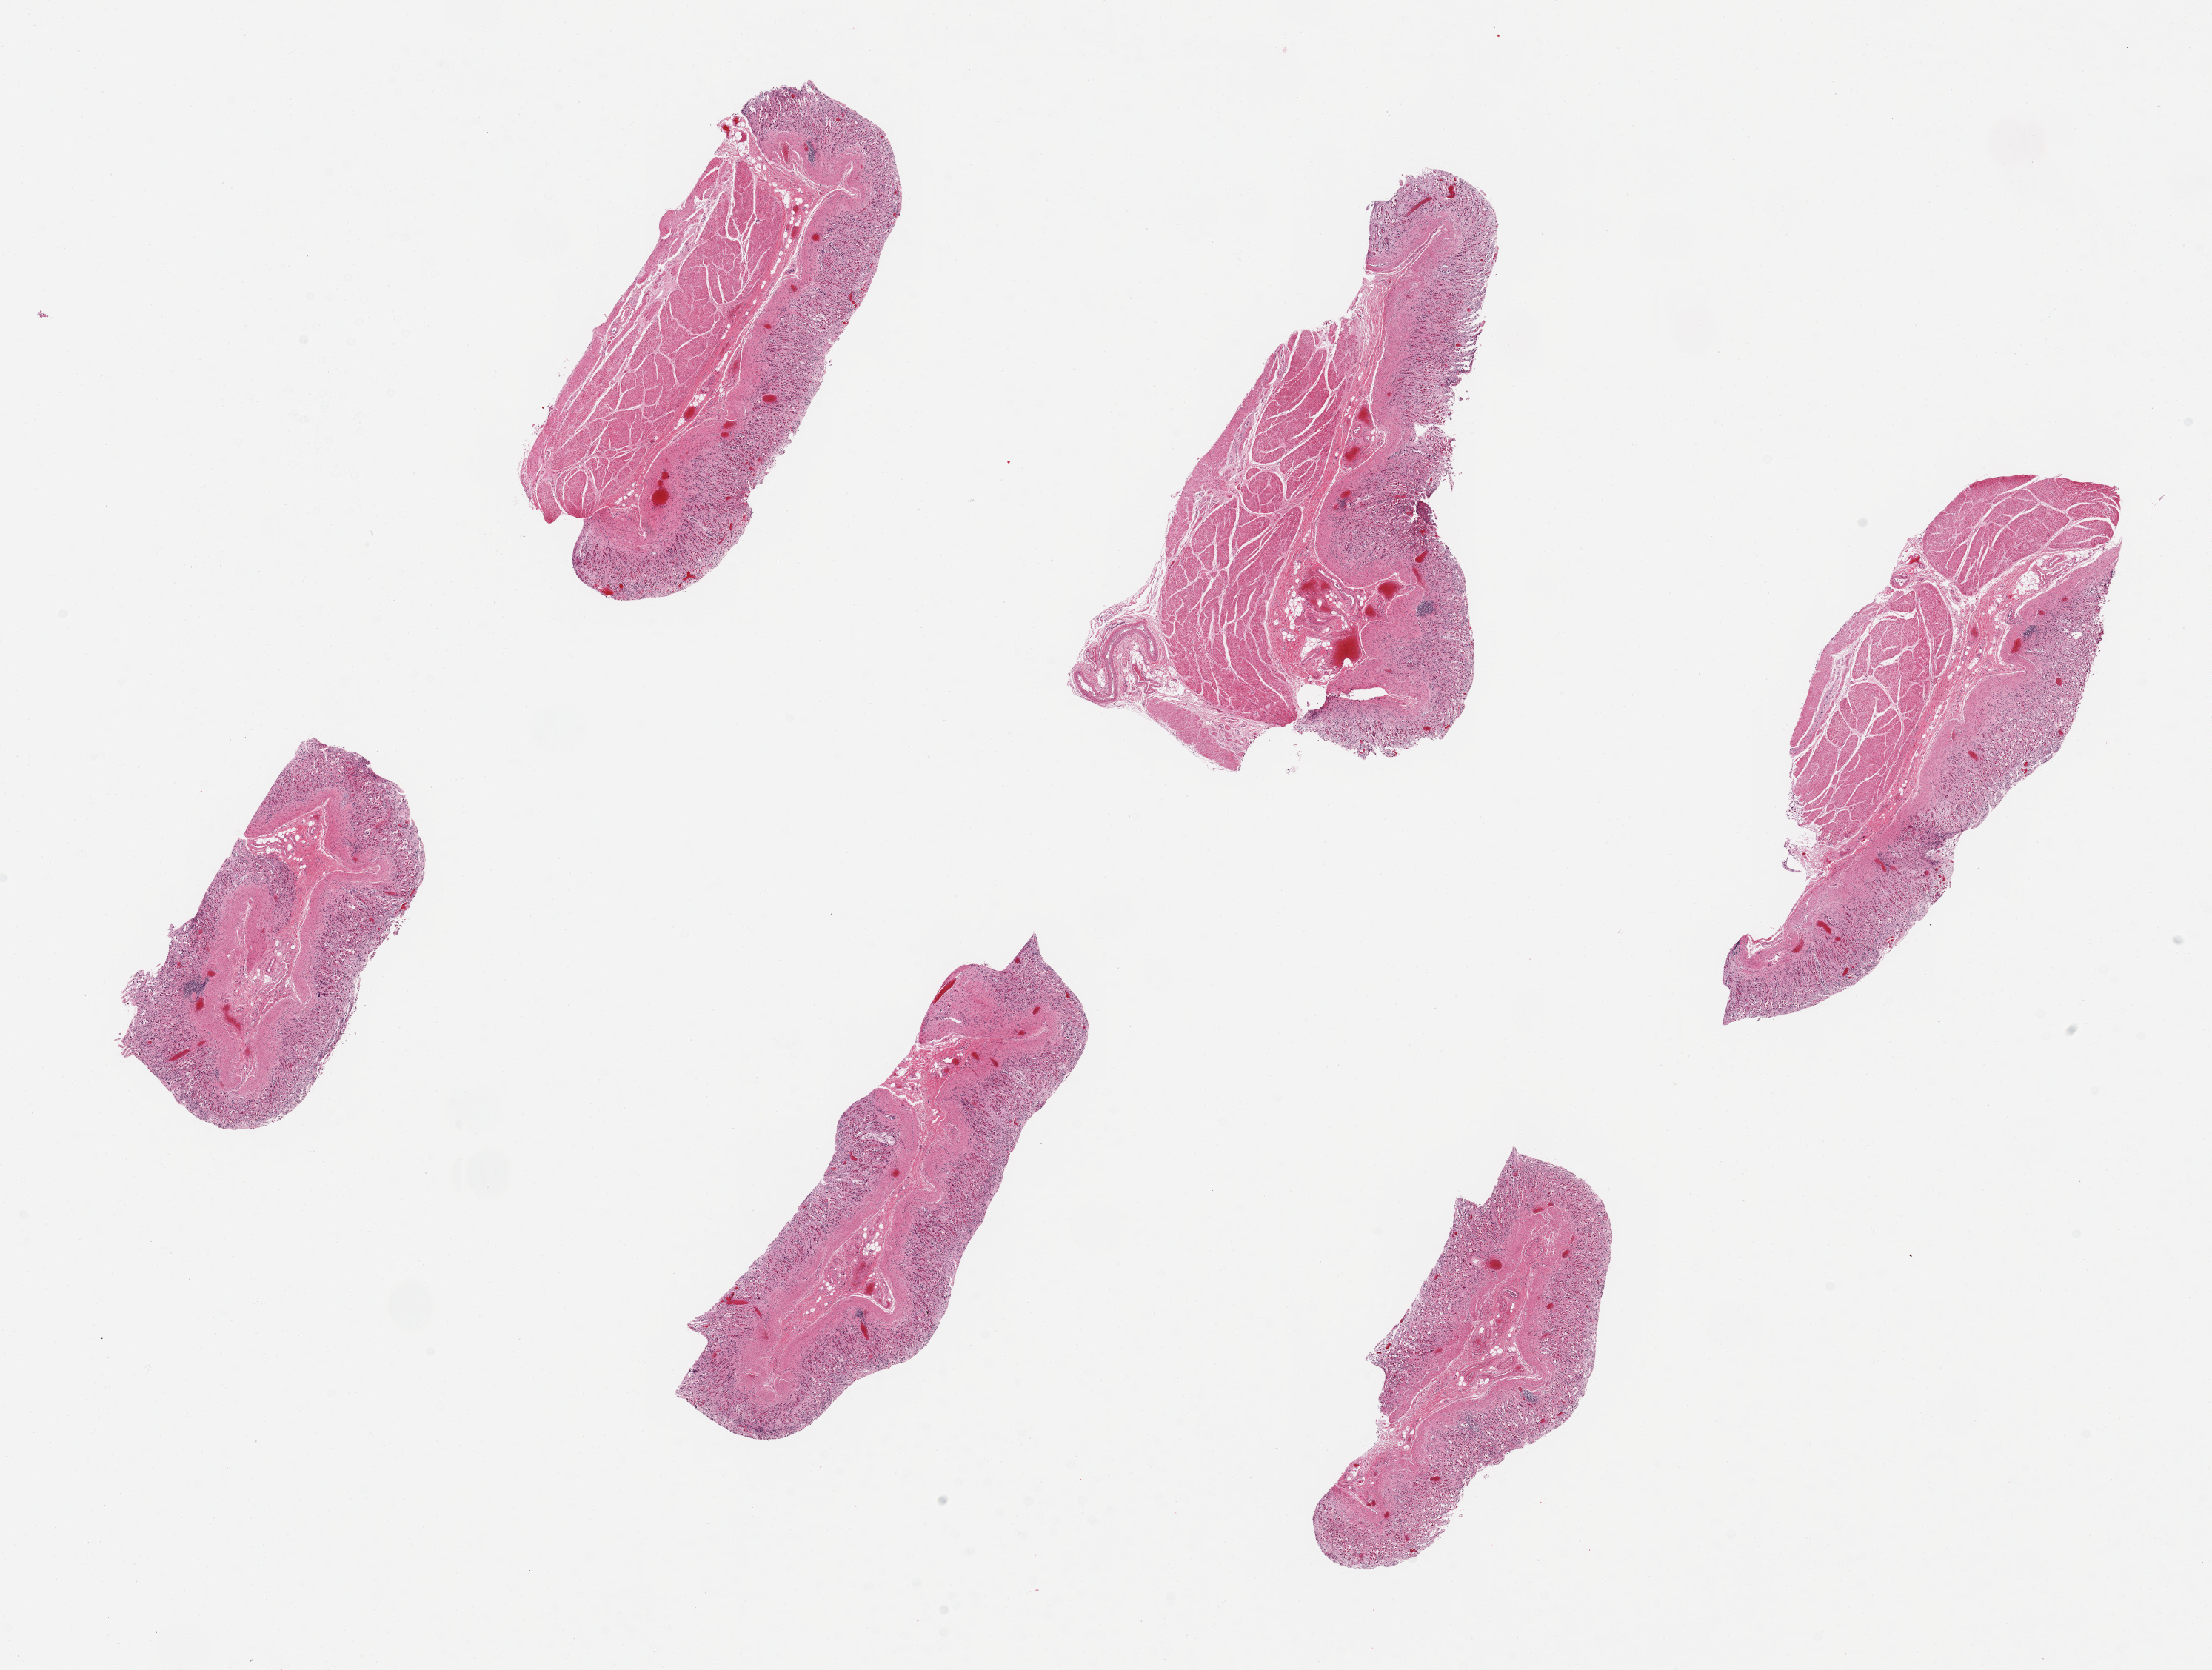
Haematoxylin and eosin whole-slide image — a low-resolution overview of the entire scanned area, about 23.6 x 17.8 mm (from a 20x scan). PAXgene-fixed paraffin-embedded (PFPE) section. Target tissue: stomach. Tissue donor sample. Female donor.
* review note (as recorded): 6 pieces up to 6.8x3.6 mm; mucosa severely autolyzed; muscle moderately autolyzed